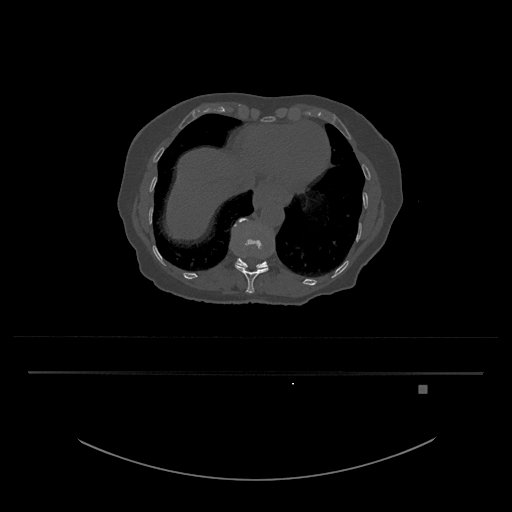
CT including the spine, one axial slice; slice 645 of 797 in the series (ordered by position); 120 kVp; bone window (W 1800 / L 400 HU); 512 × 512 image matrix, field of view 500 × 500 mm. Patient: female, 57 years. From the clinical record (not read from this slice): primary cancer: cervical.
Structures marked on this image (semi-automatic segmentation, software-assisted and operator-edited):
- T11 vertebra: bounding box <232,219,269,293> (left, top, right, bottom; pixels)
- T12 vertebra: <234,218,268,270>